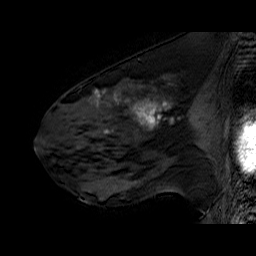
Breast MRI (dynamic contrast-enhanced), one sagittal slice. Dynamic contrast-enhanced series, time point 2 of 6 at this slice position (early post-contrast). 1.5 T. TE 6.4 ms, TR 32.9 ms. 256 × 256 image matrix, field of view 200 × 200 mm. Female patient. Case-level facts recorded for this patient, not image findings: setting: breast cancer imaged before/during neoadjuvant chemotherapy; receptor status: HER2-positive.
Annotated regions visible in this slice (semi-automatically segmented with operator editing):
- analysis volume of interest (the breast-tissue region the enhancement analysis was run in; not a lesion): box from (x=51, y=78) to (x=196, y=160) px
- tumour enhancement mask (voxels above the 100 % enhancement threshold inside the analysis volume of interest): (x=92, y=90)–(x=167, y=131)